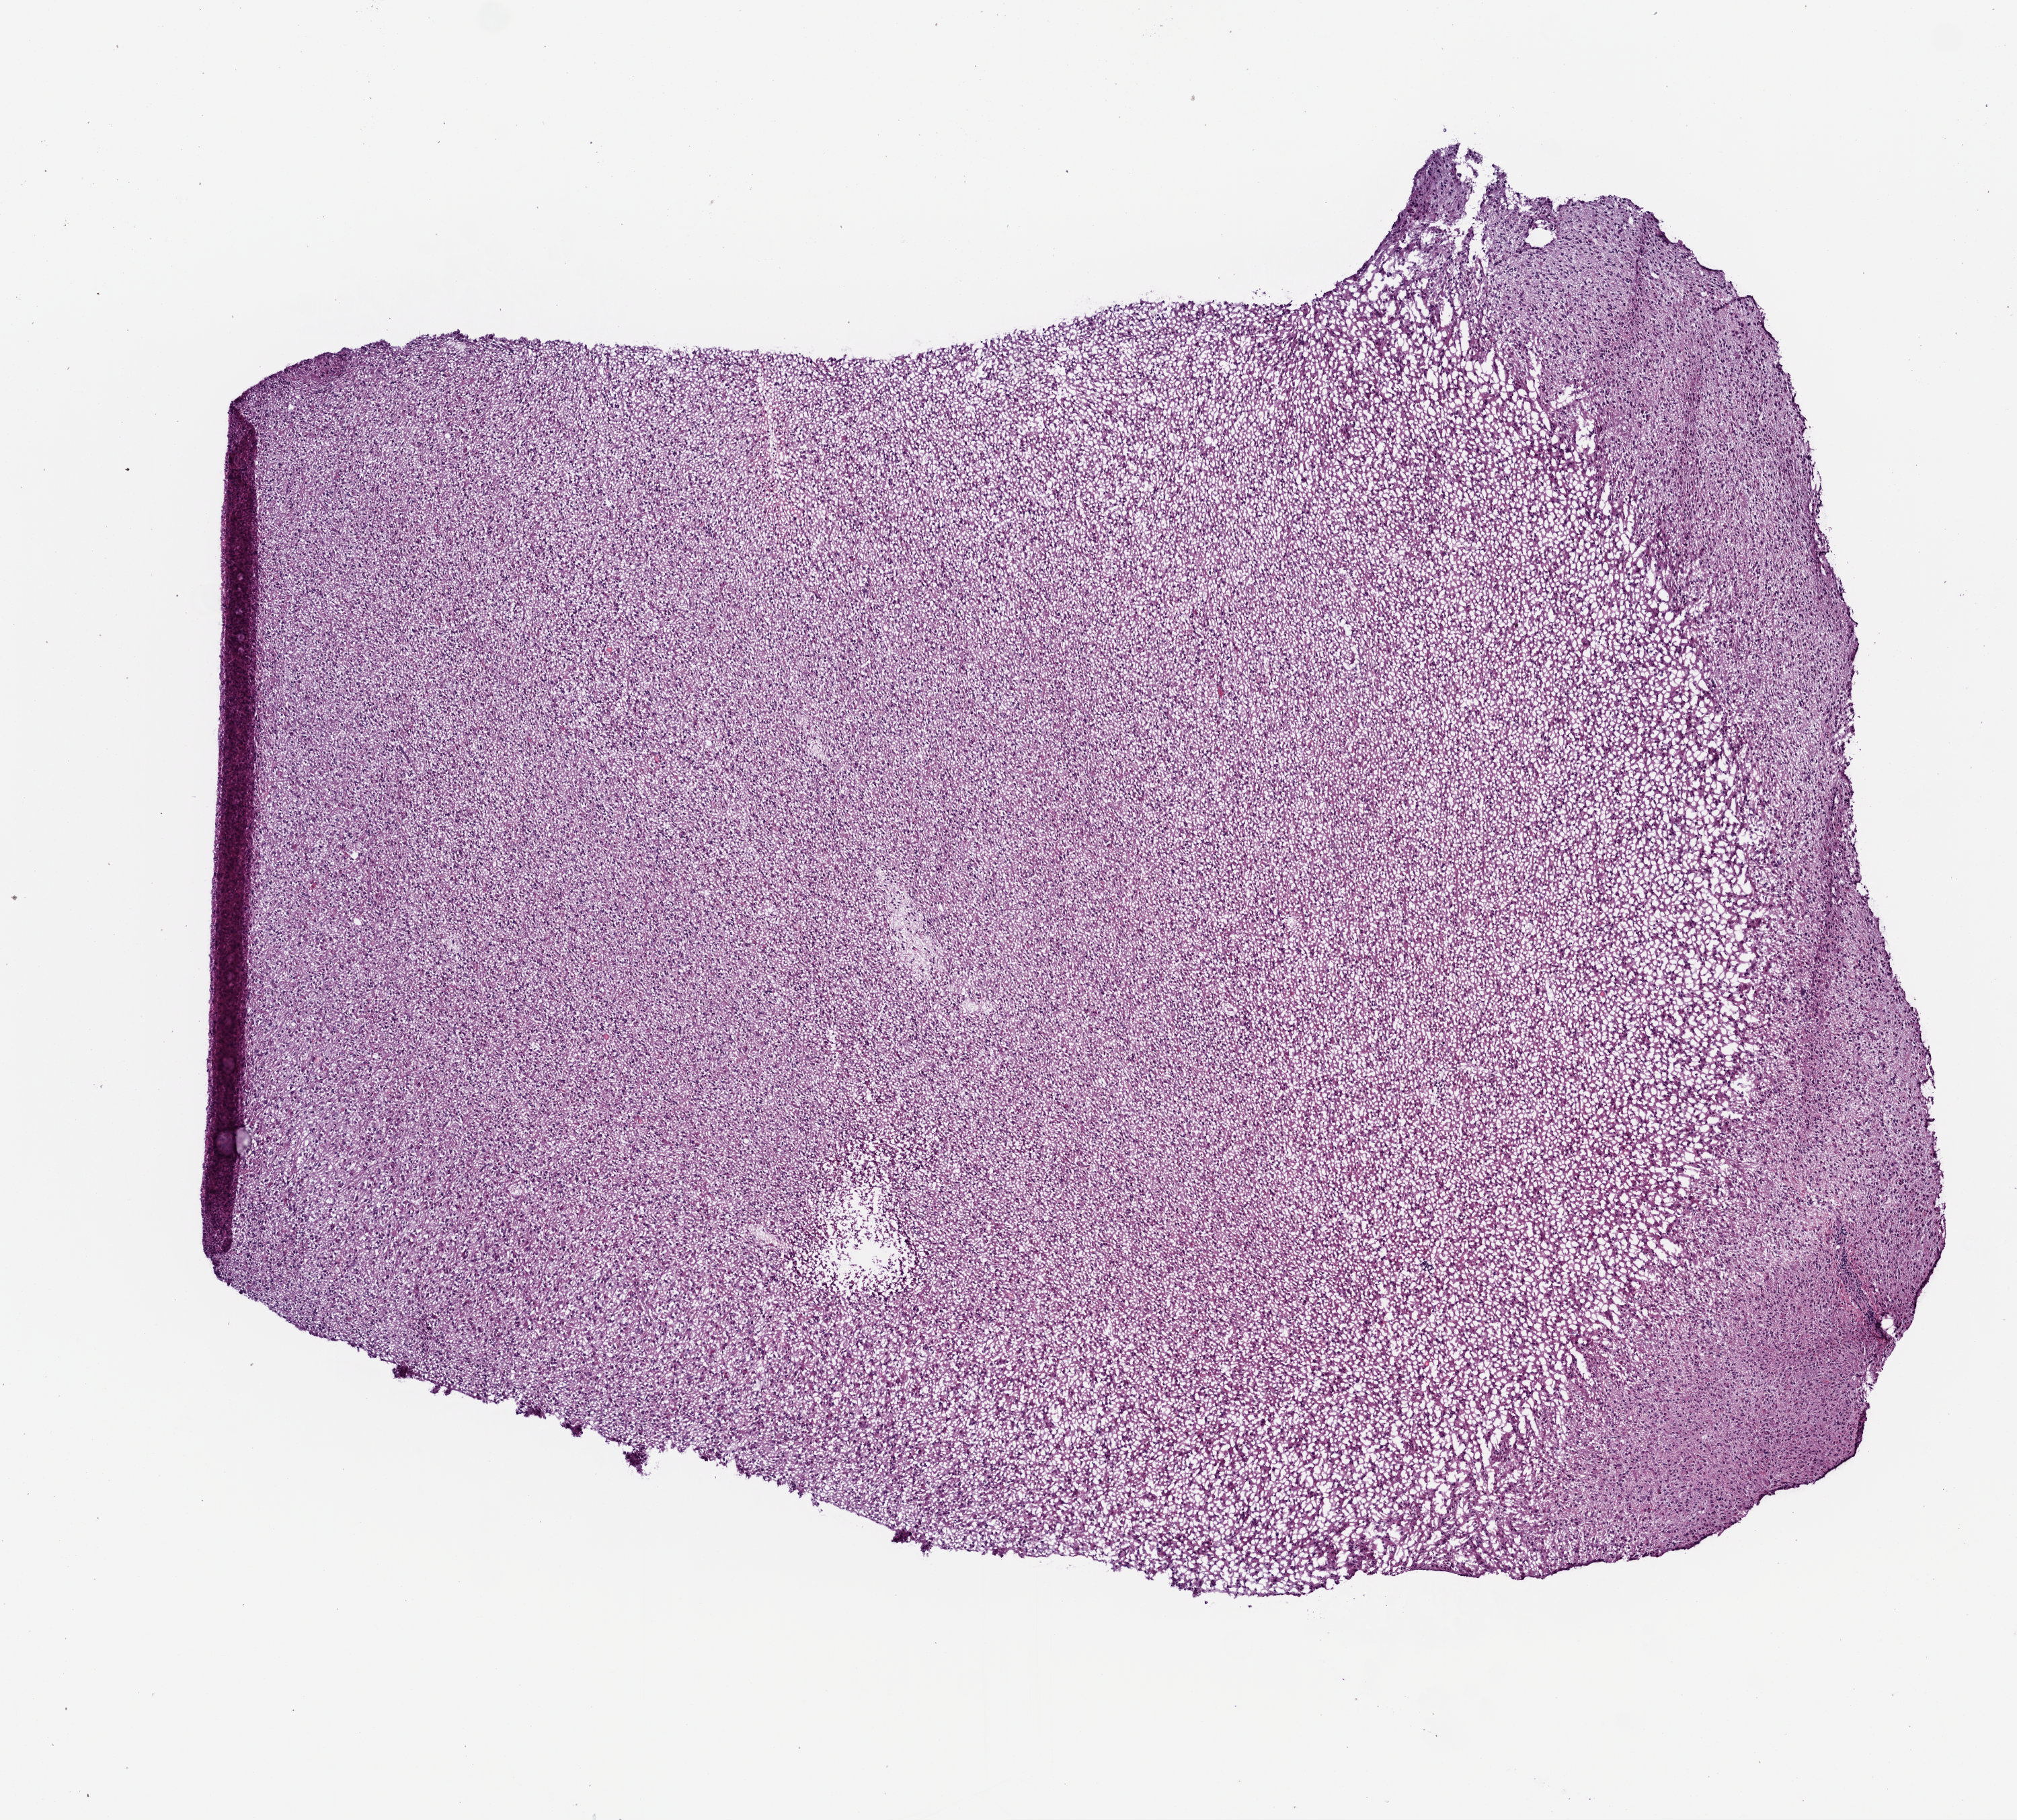
H&E-stained whole-slide image — shown as a low-resolution overview of the whole scanned area (about 6.0 x 5.4 mm), frozen section from the bottom of the tissue portion, brain, primary tumour sample. Male, age 67 years at initial diagnosis. Pathologist review of this section (percent, as recorded): tumour cells 100%, tumour nuclei 70%.
Pathologic diagnosis: Glioblastoma.